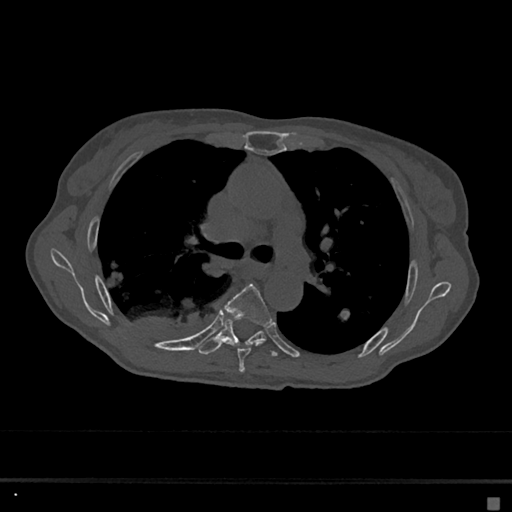
CT including the spine, one axial slice; slice 443 of 797 in the series (ordered by position); reconstruction kernel Br40s/3; 120 kVp; bone window (W 1800 / L 400 HU); 512 × 512 image matrix, field of view 360 × 360 mm. Patient: female, 68 years. From the clinical record (not read from this slice): primary cancer: renal.
Annotated regions visible in this slice (semi-automatically segmented with operator editing):
- T5 vertebra: box from (x=224, y=284) to (x=272, y=374) px
- T6 vertebra: (x=196, y=319)–(x=279, y=357)